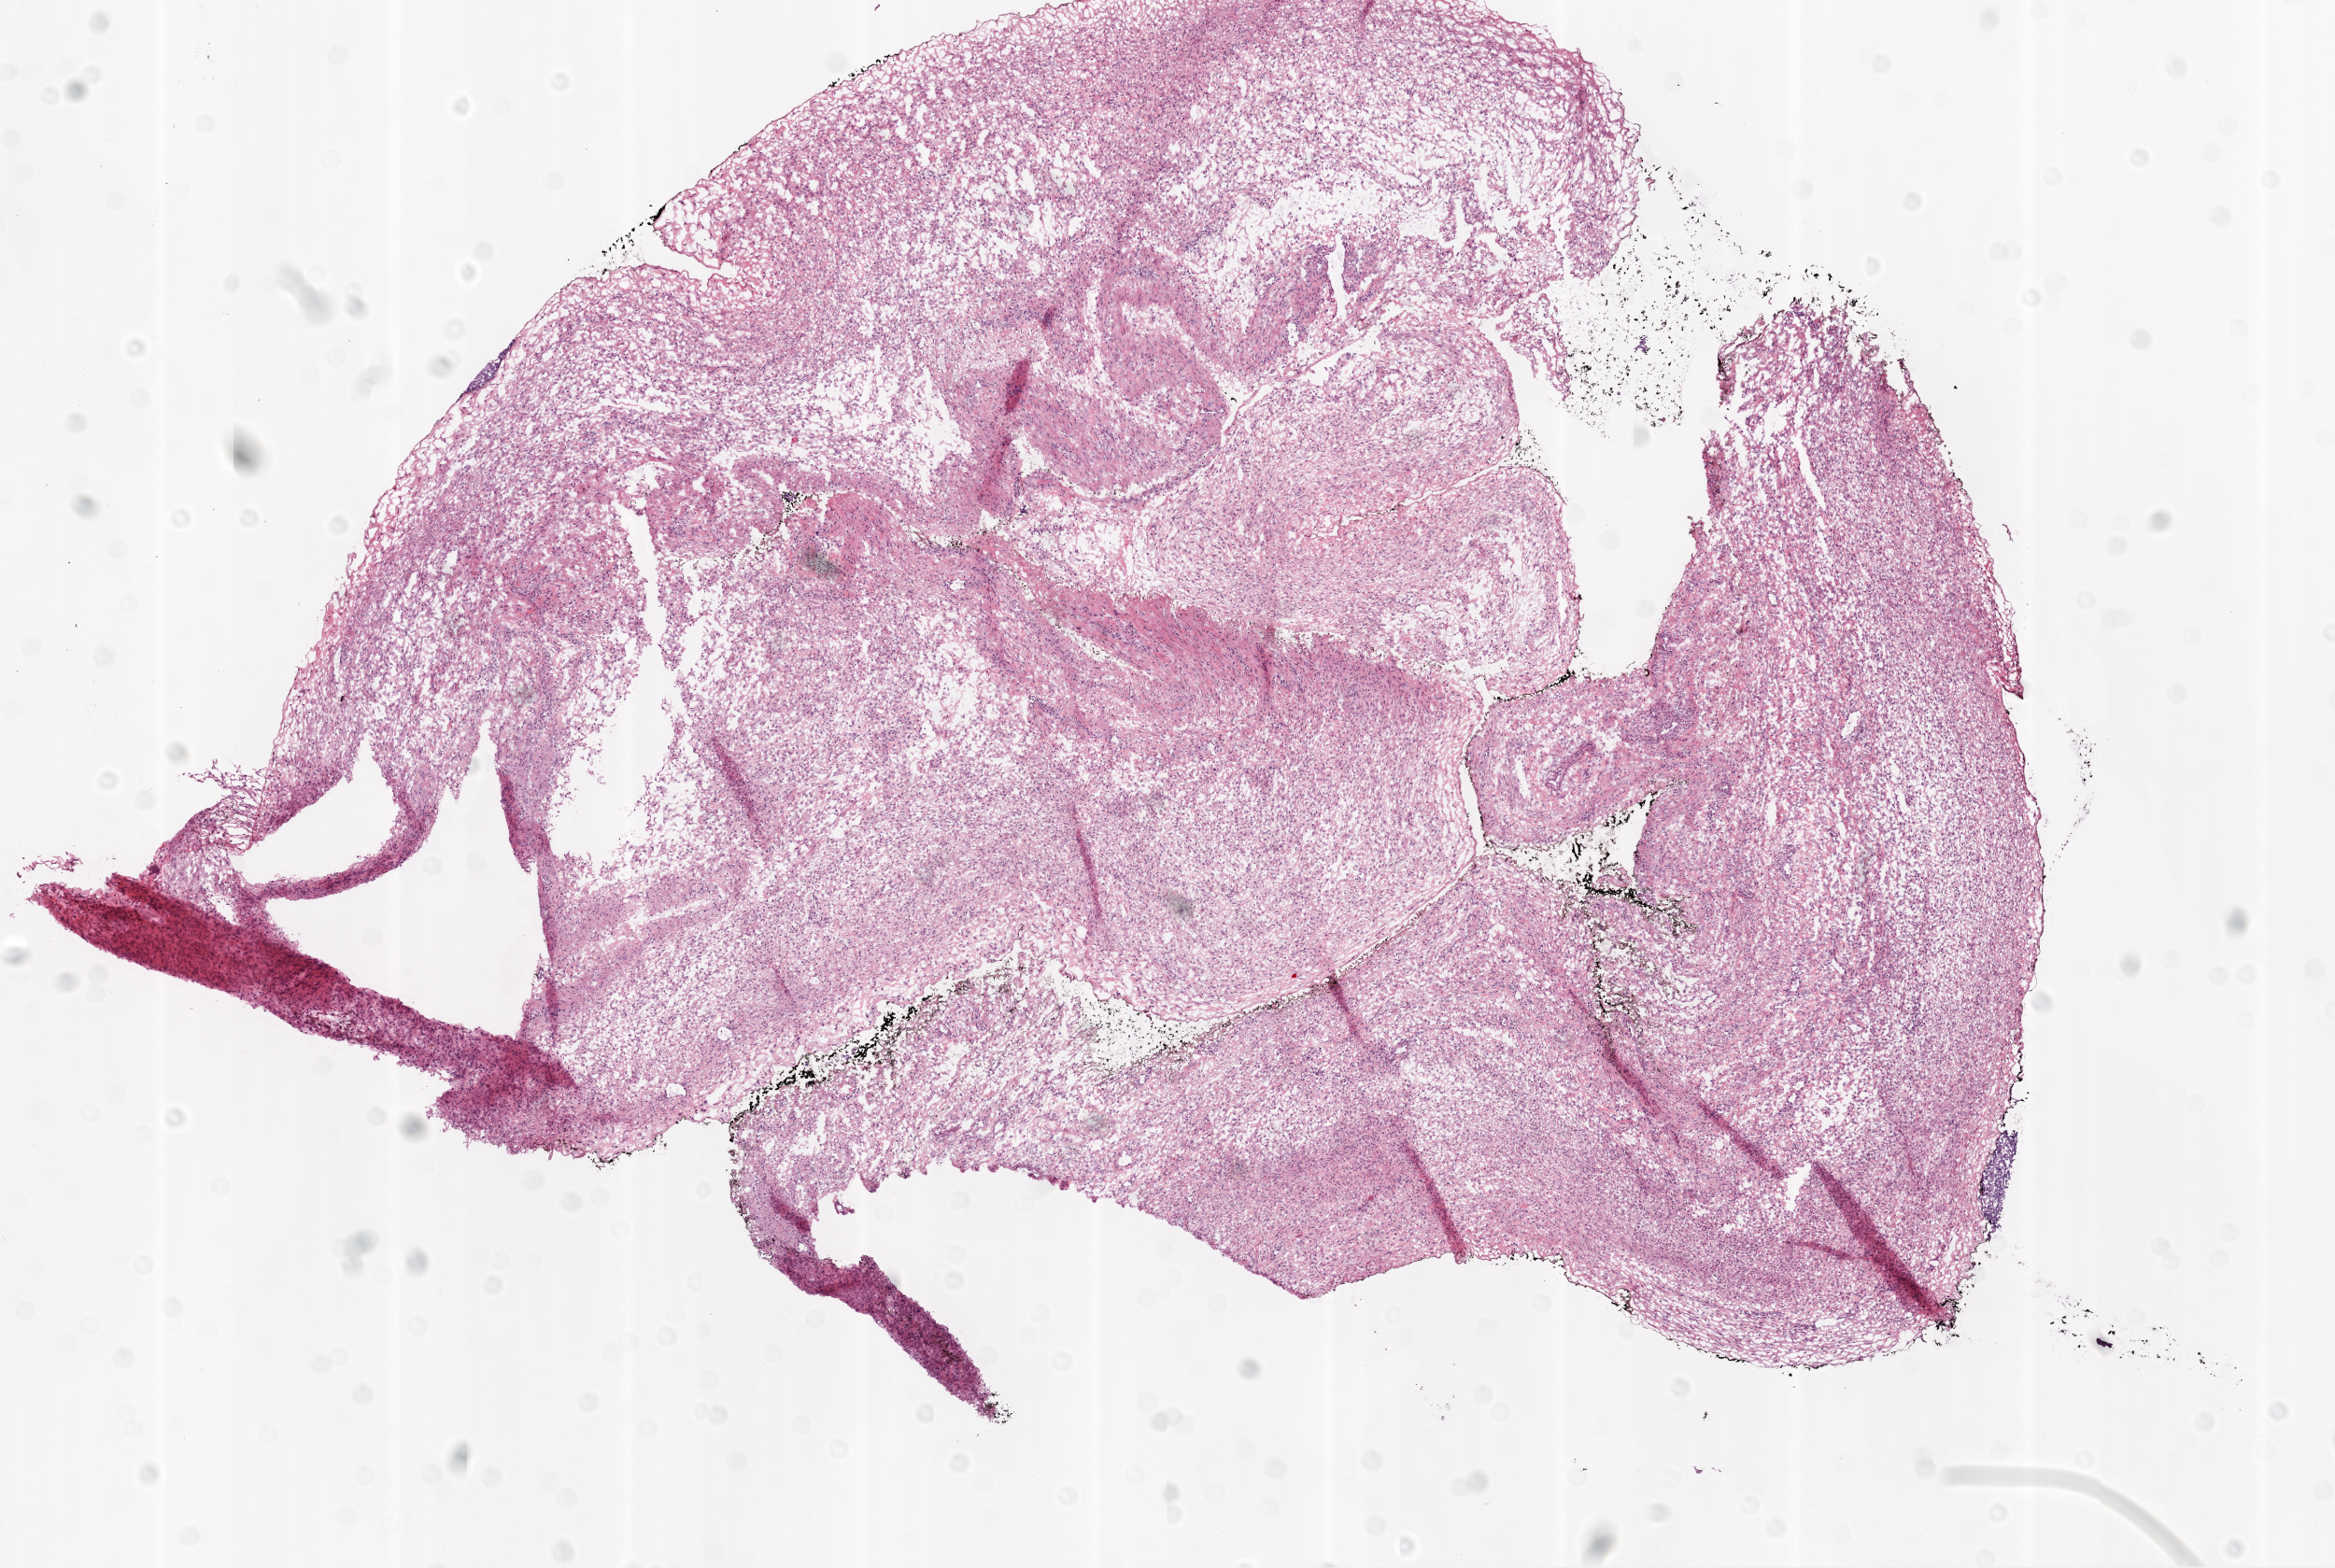
Whole-slide histology image, H&E — a low-resolution overview of the entire scanned area, about 10.0 x 6.7 mm; frozen section from the bottom of the tissue portion; sample: solid tissue normal (non-tumour tissue), ovary. Female, age 63 years at initial diagnosis.
This section: solid tissue normal (non-tumour) sample from the same patient. Patient diagnosis: Serous cystadenocarcinoma, NOS.